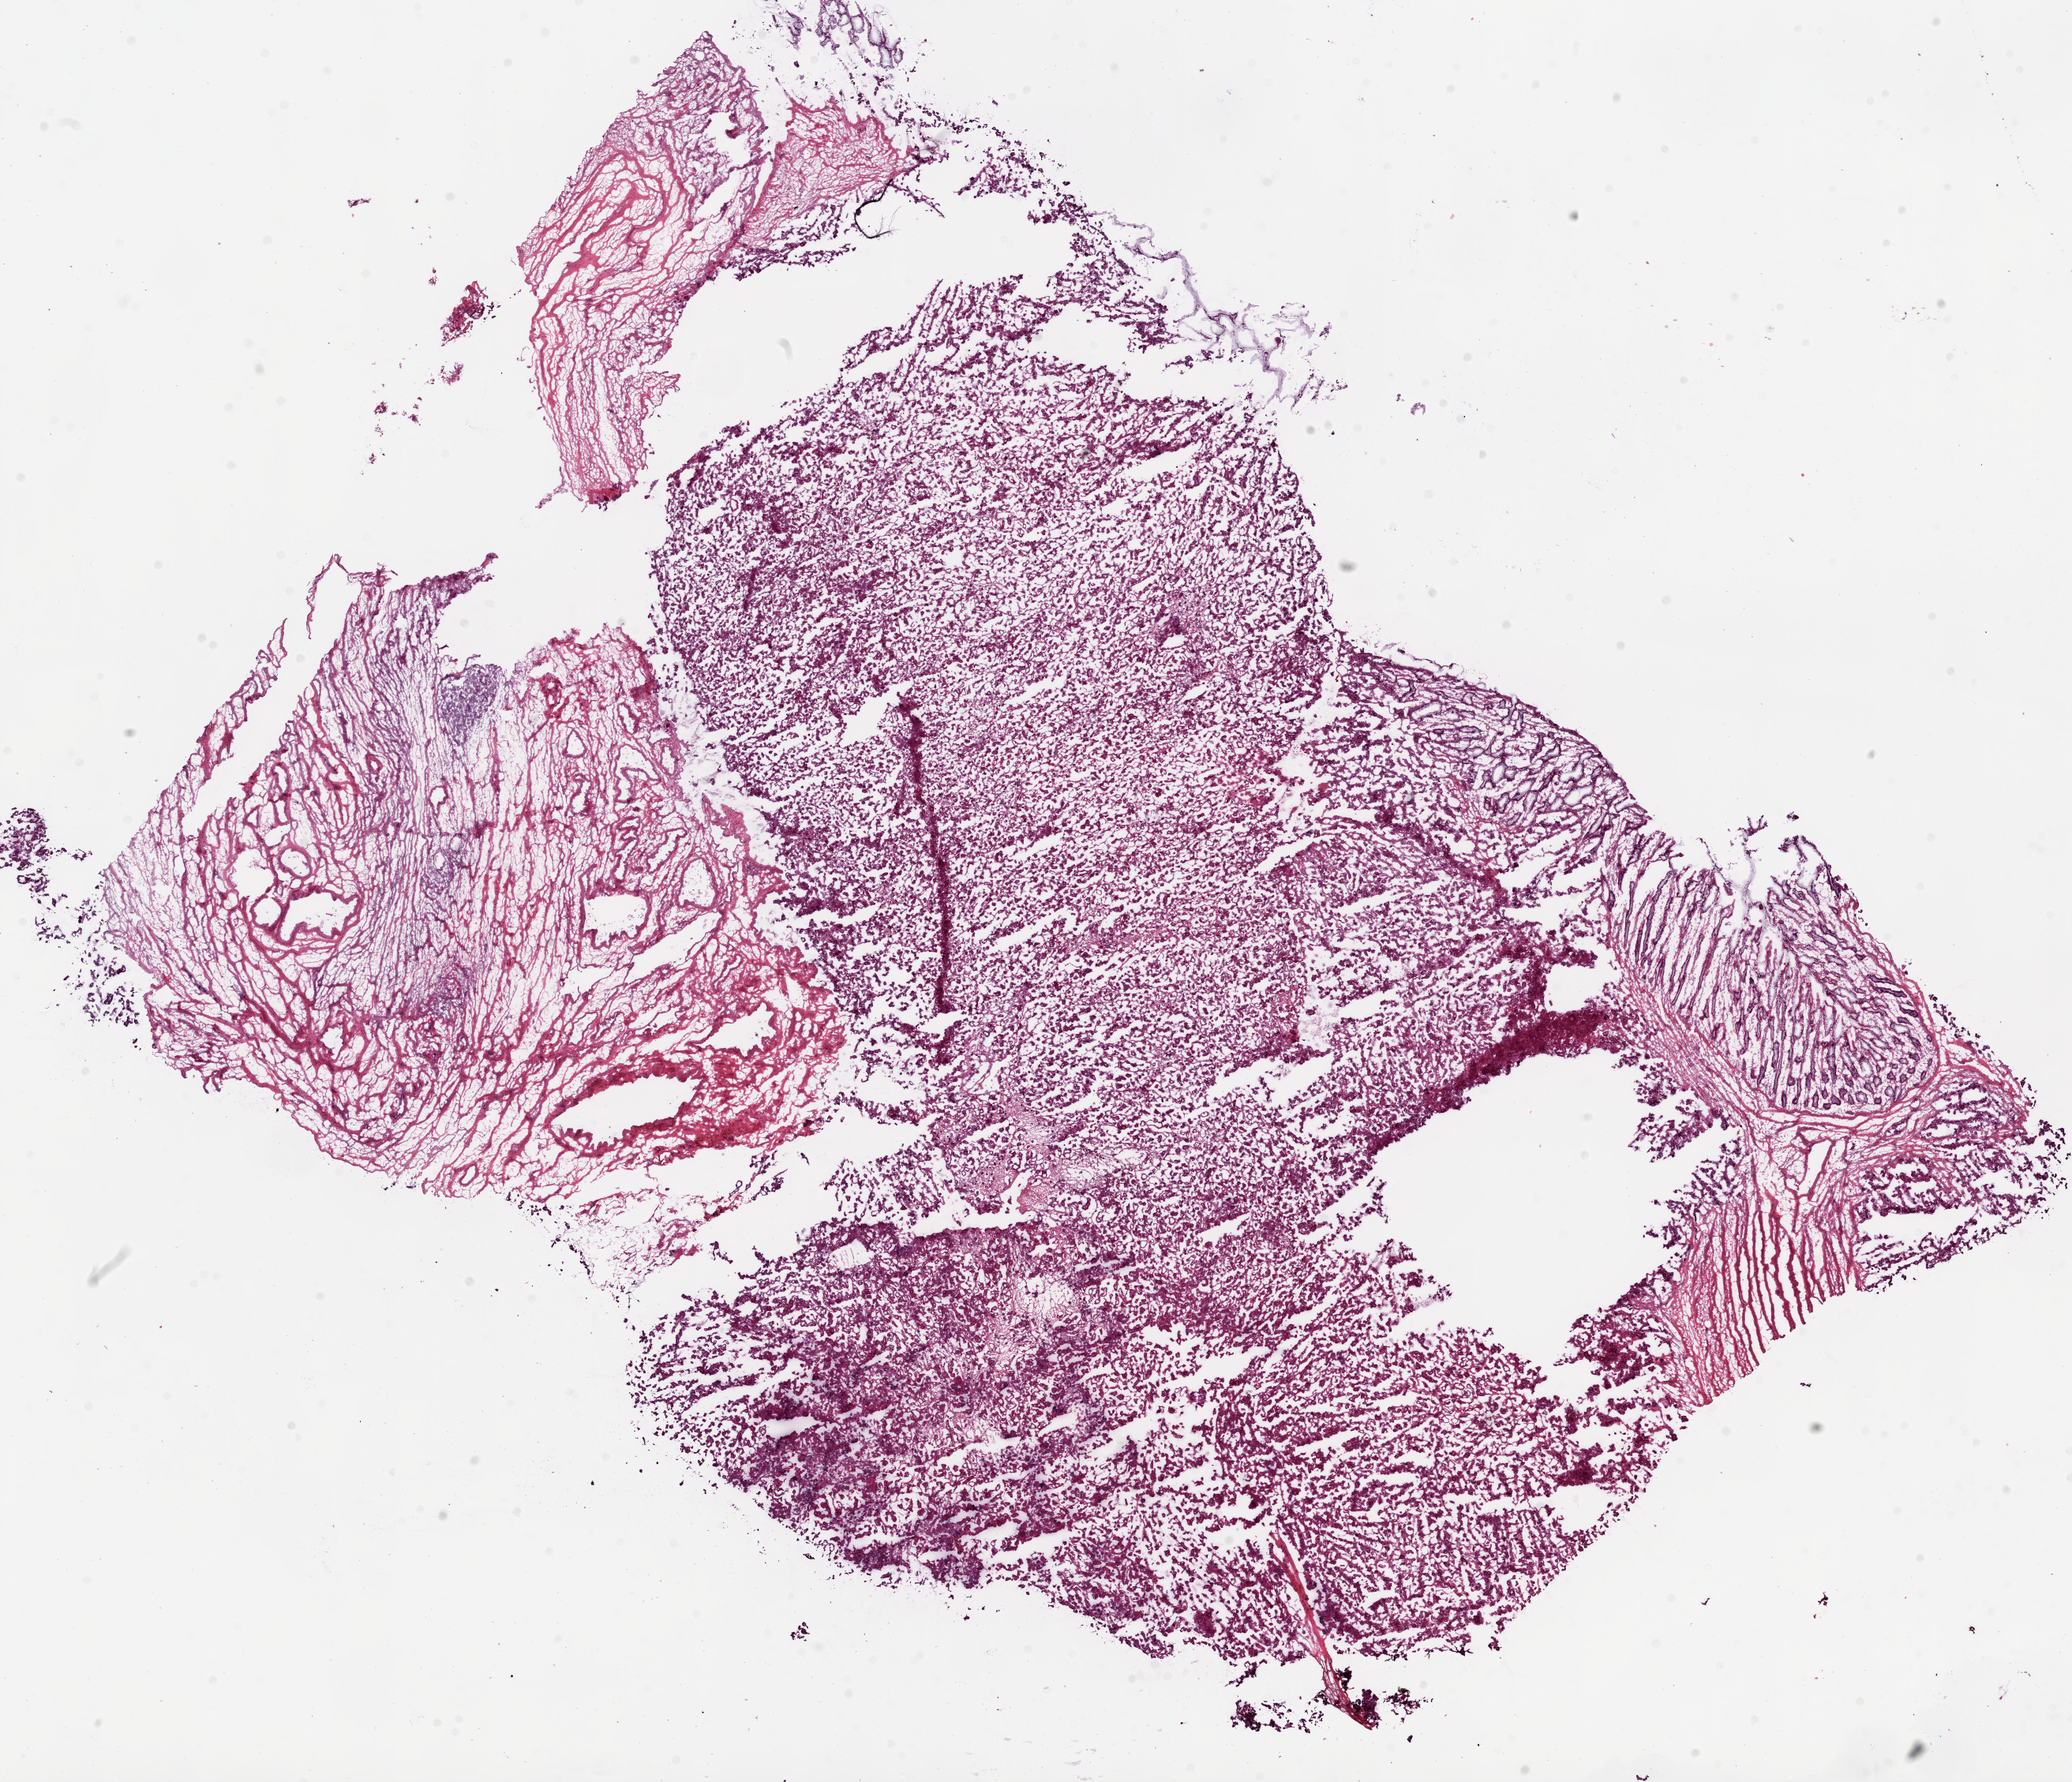
Whole-slide histology image, Hematoxylin and eosin (H&E) stained — whole scanned area (about 21.1 x 18.1 mm, slide scanned at 20x) shown as a low-resolution overview; frozen section; primary tumour sample from the ovary. Female patient; age at initial diagnosis 48 years. Histologic grade: G2 (moderately differentiated). Composition of this section per pathologist review: tumour cells 70%, tumour nuclei 80%, normal cells 0%, stromal cells 30%, necrosis 0%.
• FIGO stage: IV
• laterality: bilateral
• pathologic diagnosis: Serous cystadenocarcinoma, NOS